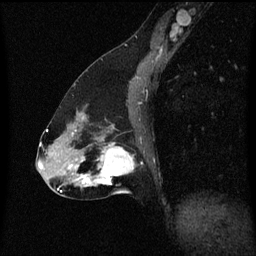
Breast MRI (dynamic contrast-enhanced), one sagittal slice; dynamic contrast-enhanced series, image 2 of 3 at this slice position (ordered by acquisition); 1.5 T; TE 4.2 ms, TR 8.4 ms; 2 mm slice thickness; 256 × 256 image matrix, field of view 200 × 200 mm. Patient: female, 47 years.
Outlined on this slice (semi-automatic segmentation, software-assisted and operator-edited):
- analysis volume of interest (the breast-tissue region the enhancement analysis was run in; not a lesion): bounding box [x1, y1, x2, y2] px = [85, 136, 134, 195]
- tumour enhancement mask (voxels above the 70 % enhancement threshold inside the analysis volume of interest): [85, 144, 134, 185]